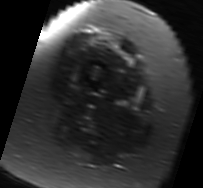
MRI of an extremity soft-tissue mass, one axial slice. Slice 9 of 91 in the series (ordered by position). T2-weighted fat-saturated. MR volume resampled by the dataset authors to the PET/CT grid (not the native acquisition matrix). 3.27 mm slice thickness. 203 × 188 image matrix. Female patient. Case-level facts recorded for this patient, not image findings: histological type: malignant solitary fibrous tumor; grade: intermediate; site of the primary tumour: right thigh.
Outlined on this slice (expert contour drawn on MRI and transferred to this co-registered scan by the dataset authors):
- gross tumour volume including surrounding oedema: bounding box [x1, y1, x2, y2] px = [119, 50, 121, 52]